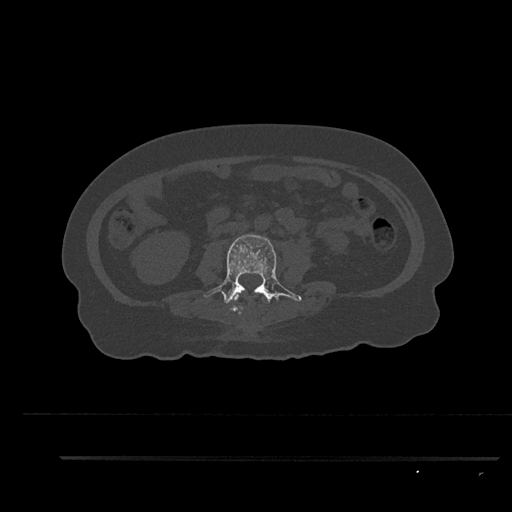
CT including the spine, one axial slice. Slice 97 of 797 in the series (ordered by position). Reconstruction kernel Br40s/3. 120 kVp. Bone window (W 1800 / L 400 HU). 512 × 512 image matrix, field of view 408 × 408 mm. Patient: female, 44 years. From the clinical record (not read from this slice): primary cancer: renal; vertebrae with lytic lesions (as recorded): L1.
Outlined on this slice (semi-automatically segmented with operator editing):
- L2 vertebra: box from (x=231, y=294) to (x=264, y=315) px
- L3 vertebra: (x=204, y=234)–(x=302, y=312)